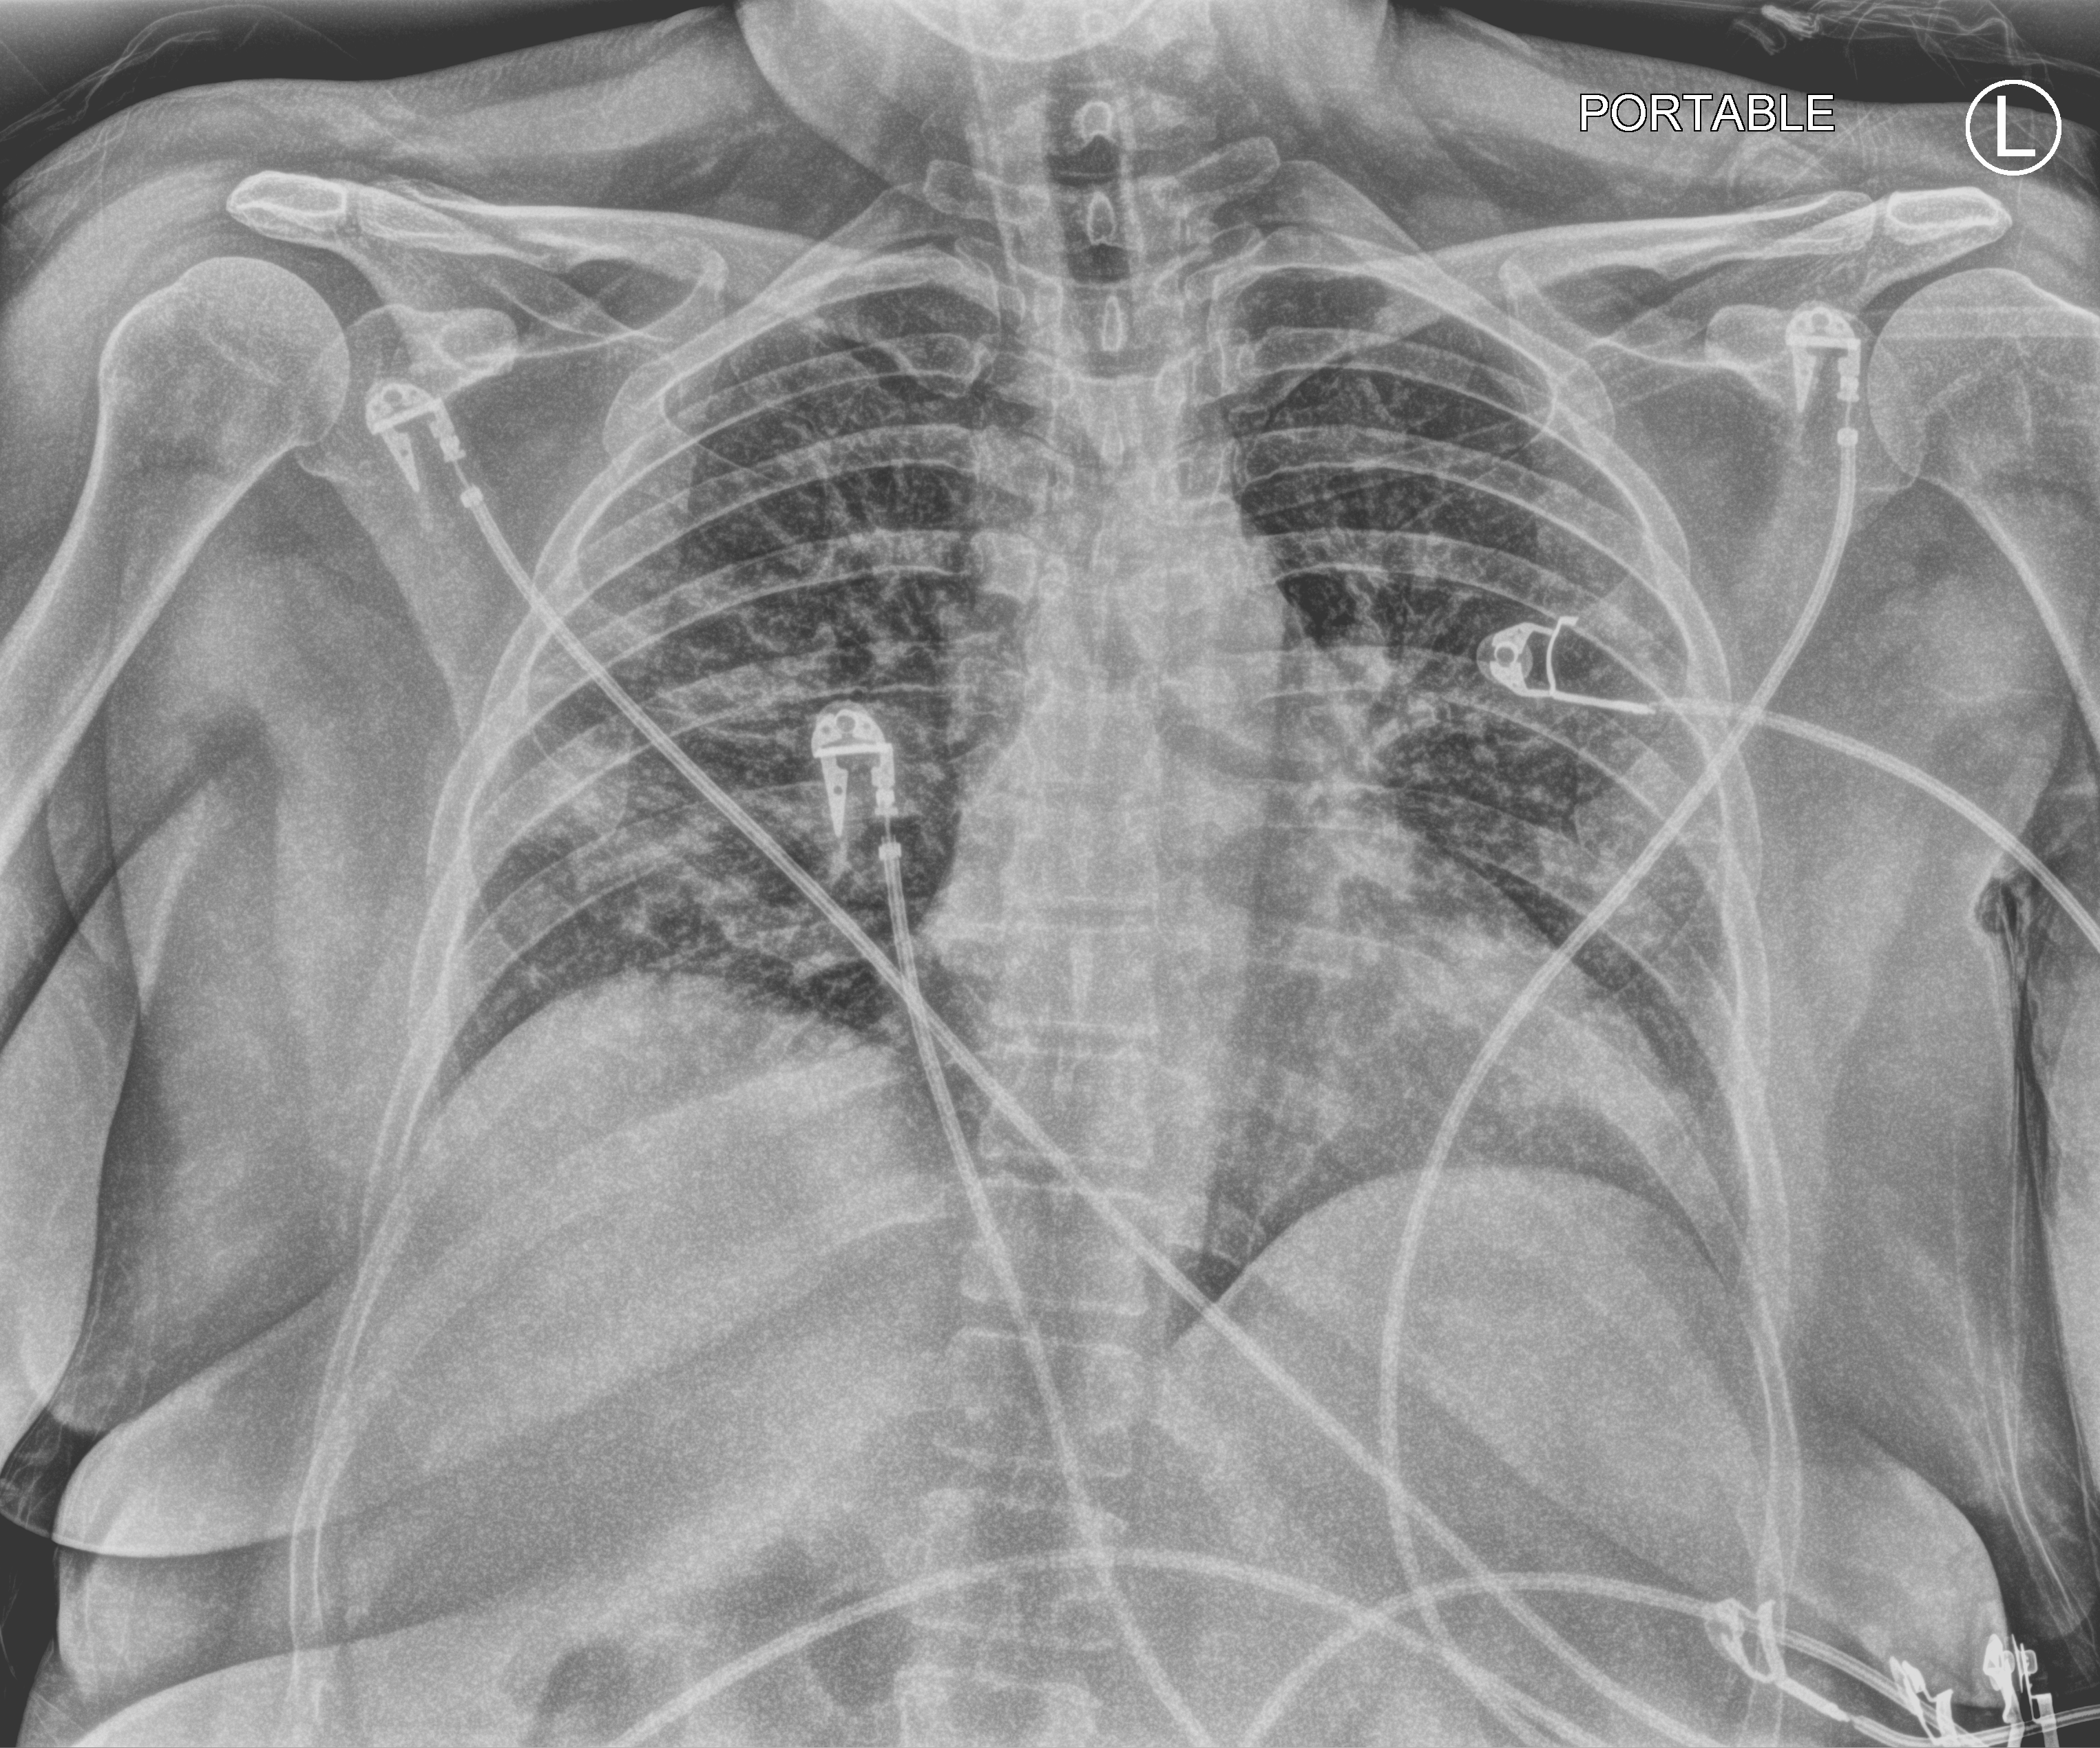
Chest X-ray (portable); anteroposterior (AP) projection. Patient hospitalised with COVID-19; female, aged 18–59 years.
Admission-level facts for this patient (not findings on this image; timing relative to this image not recorded): length of hospital stay: 31 days; chronic kidney disease (admission record): no; mechanically ventilated during this hospital stay: yes.